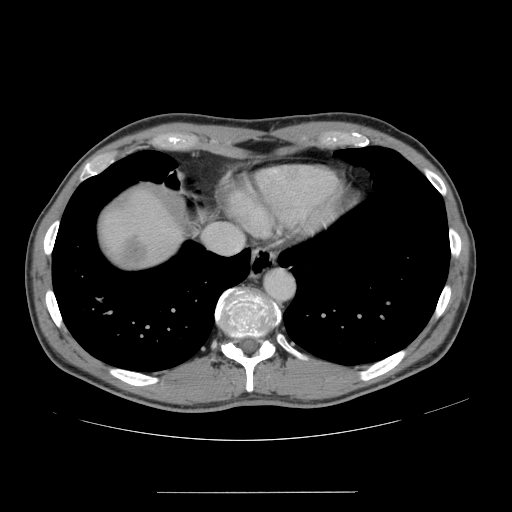
Contrast-enhanced abdominal CT, one axial slice. Slice 141 of 178 in the series (ordered by position). Intravenous contrast given. Soft-tissue window (W 400 / L 40 HU). 512 × 512 image matrix, field of view 401 × 401 mm. Male patient, age 53 years. From the clinical record (not read from this slice): diagnosis: colorectal cancer liver metastases, imaged before liver resection; multiple liver metastases: yes; largest metastasis: 2.4 cm; disease in both lobes: no.
Outlined on this slice (manually delineated by an expert):
- liver: bounding box [x1, y1, x2, y2] px = [99, 189, 182, 267]
- liver metastasis: [119, 235, 148, 264]